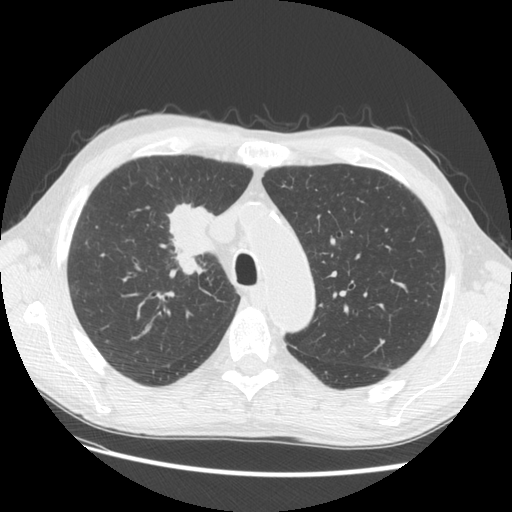
Low-dose screening chest CT, one axial slice. Position 99 of 133 along the scan axis. Lung window (W 1500 / L -600 HU). 2.5 mm slice thickness. 512 × 512 image matrix.
Structures marked on this image (expert manual segmentation):
- lesion 1 (tumor, hilum of right lung): bounding box [x1, y1, x2, y2] px = [166, 202, 217, 275]